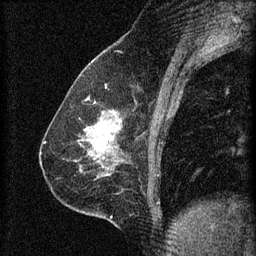
Breast MRI (dynamic contrast-enhanced), one sagittal slice; slice 26 of 60 in the series (ordered by position); 3 images stored at this slice position (order not interpretable as contrast timing); 1.5 T; TE 4.2 ms, TR 8.2 ms; 2 mm slice thickness; 256 × 256 image matrix, field of view 180 × 180 mm. Patient: female, 59 years.
Annotated regions visible in this slice (semi-automatically segmented with operator editing):
- analysis volume of interest (the breast-tissue region the enhancement analysis was run in; not a lesion): bounding box <61,106,126,161> (left, top, right, bottom; pixels)
- tumour enhancement mask (voxels above the 70 % enhancement threshold inside the analysis volume of interest): <86,124,117,145>